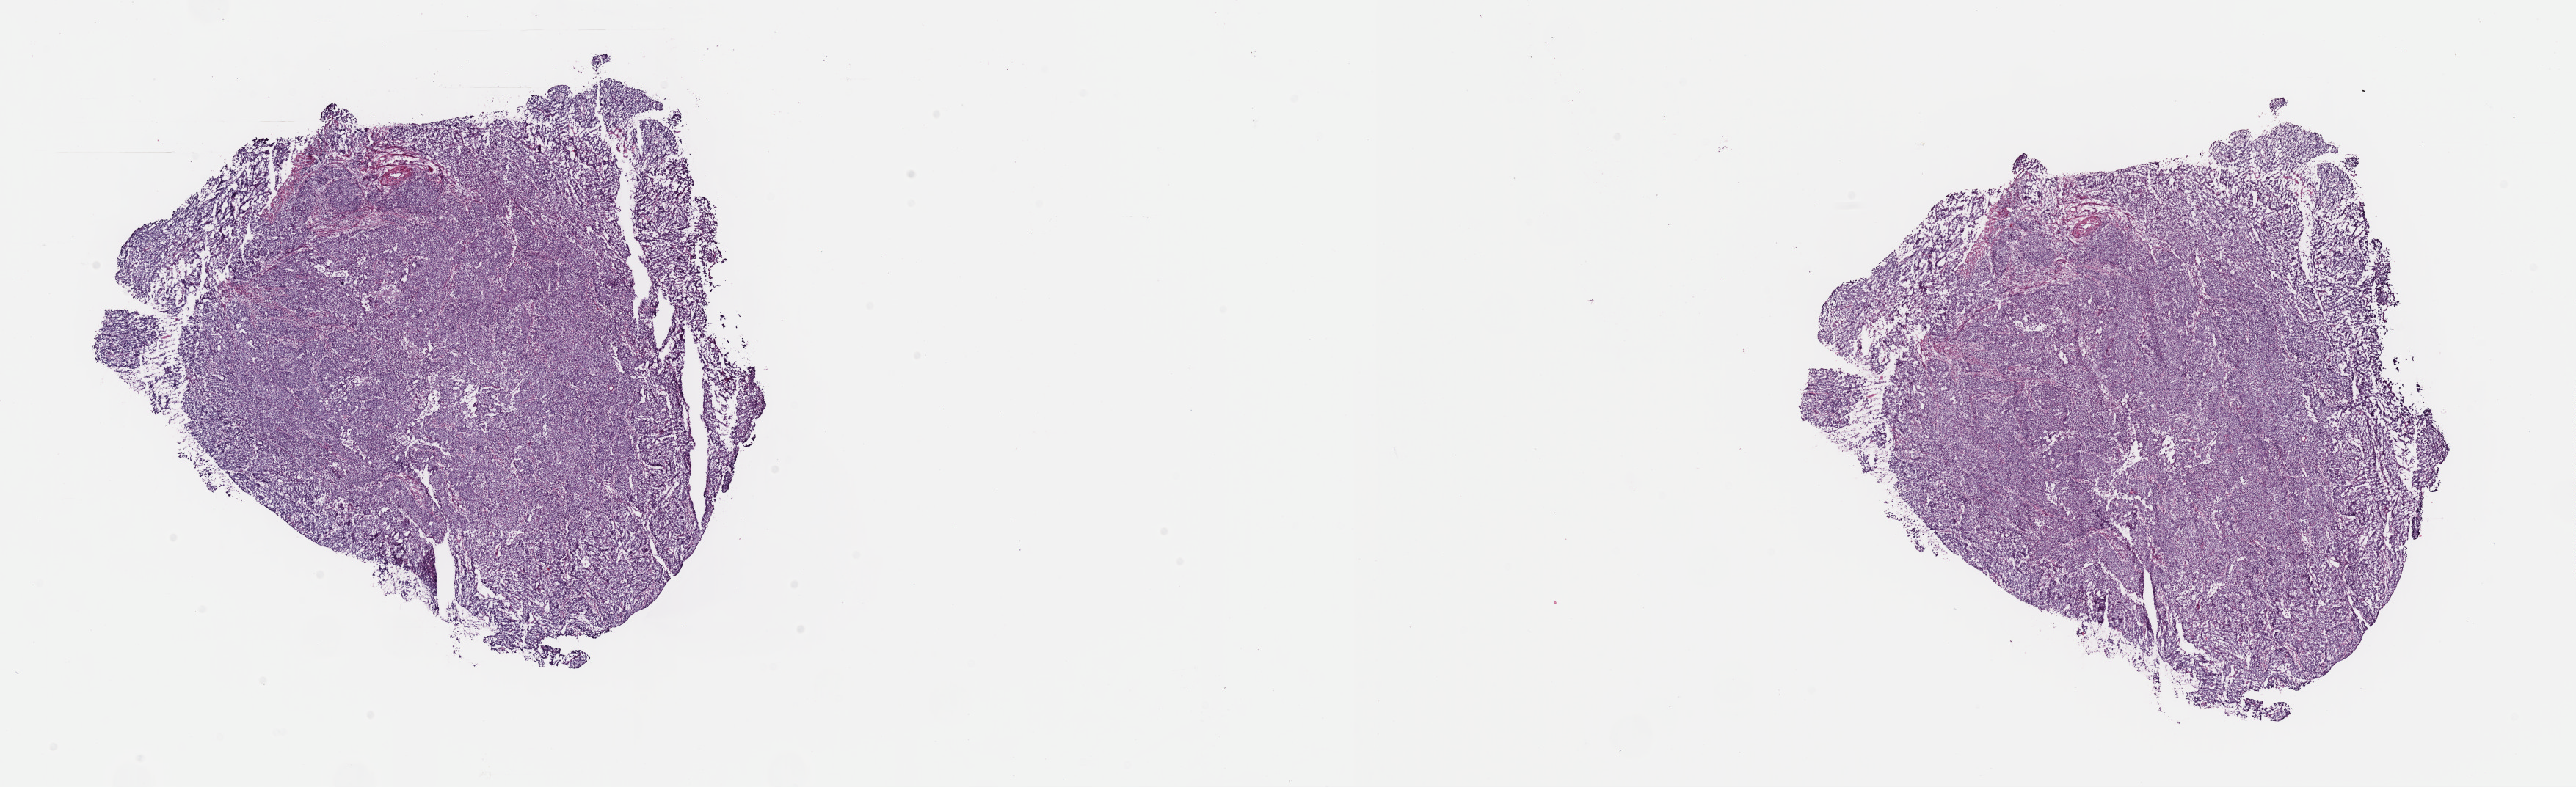
Whole-slide histology image, H&E, shown as a low-resolution overview of the whole scanned area (about 27.7 x 8.5 mm). Frozen section from the top of the tissue portion. Primary tumour sample from the uterus. Female patient; age at initial diagnosis 58 years. Histologic grade: G3 (poorly differentiated). Composition of this section per pathologist review: tumour cells 90%, tumour nuclei 90%, normal cells 0%, stromal cells 8%, necrosis 2%. Infiltration values recorded for this section: lymphocyte infiltration 0%, monocyte infiltration 0%, neutrophil infiltration 0%.
FIGO stage: IB. Diagnosis: Endometrioid adenocarcinoma, NOS (endometrium).